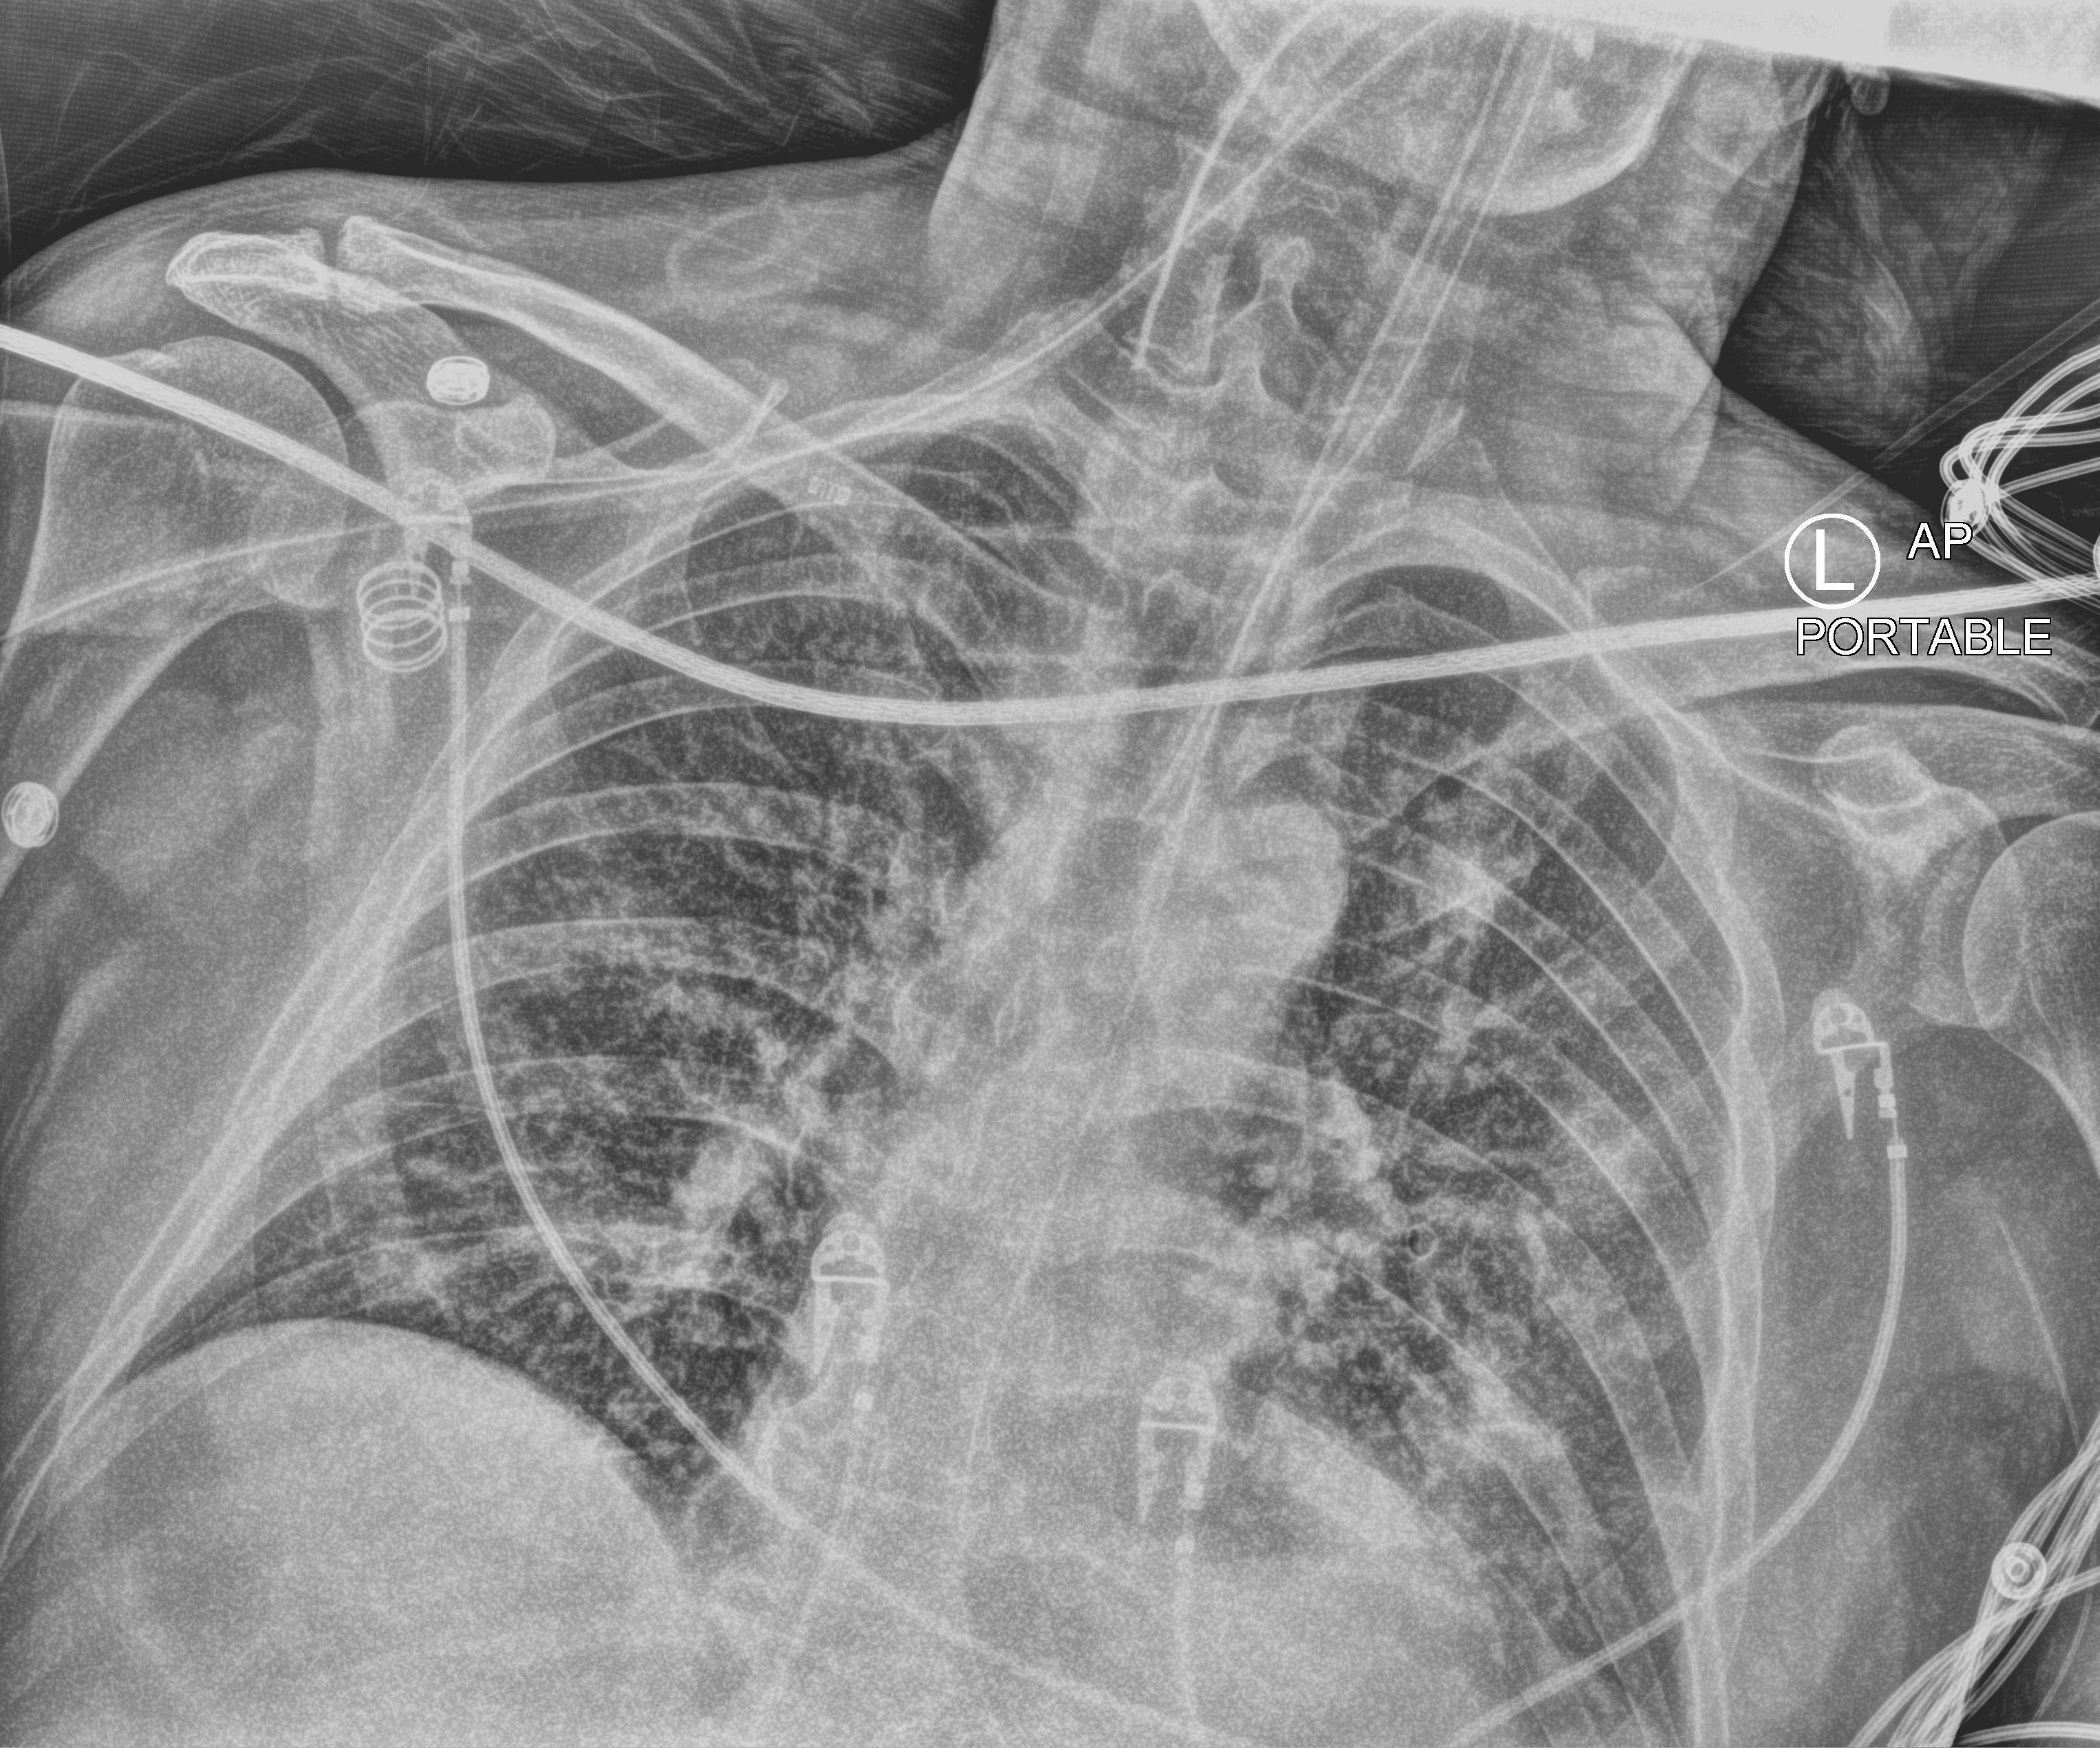
Bedside chest radiograph (computed radiography), anteroposterior (AP) projection. Patient hospitalised with COVID-19; male, aged 18–59 years.
Admission-level facts for this patient (not findings on this image; timing relative to this image not recorded): mechanically ventilated during this hospital stay: yes.